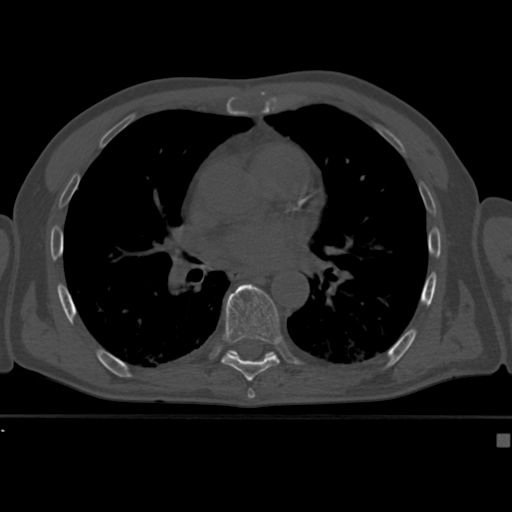
CT including the spine, one axial slice. Slice 261 of 430 in the series (ordered by position). Reconstruction kernel Br40s. Bone window (W 1800 / L 400 HU). 512 × 512 image matrix, field of view 337 × 337 mm. Male patient, age 64 years. Case-level facts recorded for this patient, not image findings: primary cancer: uterus.
Annotated regions visible in this slice (semi-automatically segmented with operator editing):
- T8 vertebra: bounding box <222,283,281,382> (left, top, right, bottom; pixels)
- T9 vertebra: <227,349,276,358>